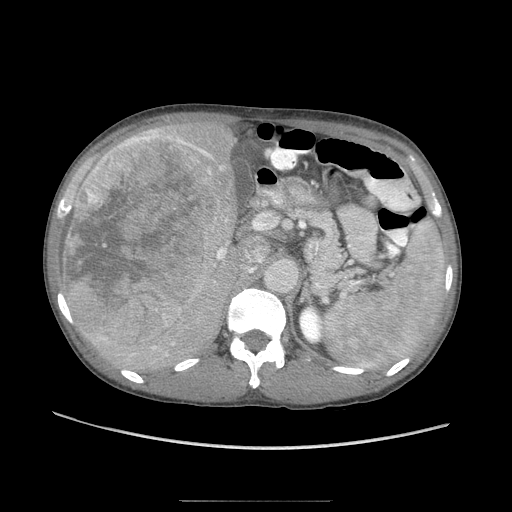
Contrast-enhanced abdominal CT (liver protocol), one axial slice; slice 52 of 103 in the series (ordered by position); reconstruction kernel STANDARD; 120 kVp; soft-tissue window (W 400 / L 40 HU); 512 × 512 image matrix. Case-level facts recorded for this patient, not image findings: diagnosis: hepatocellular carcinoma (patient treated with transarterial chemoembolisation; whether this scan precedes or follows treatment is not stated here); TNM stage (as recorded): Stage-IIIA; Child-Pugh class: A; tumour differentiation: moderately differentiated.
Annotated regions visible in this slice (semi-automatic segmentation, software-assisted and operator-edited):
- liver parenchyma outside the tumour (the mass and vessels are separate outlines, so this box may not span the whole liver): bounding box <72,116,251,374> (left, top, right, bottom; pixels)
- mass: <62,118,234,345>
- liver vessels: <100,138,218,266>